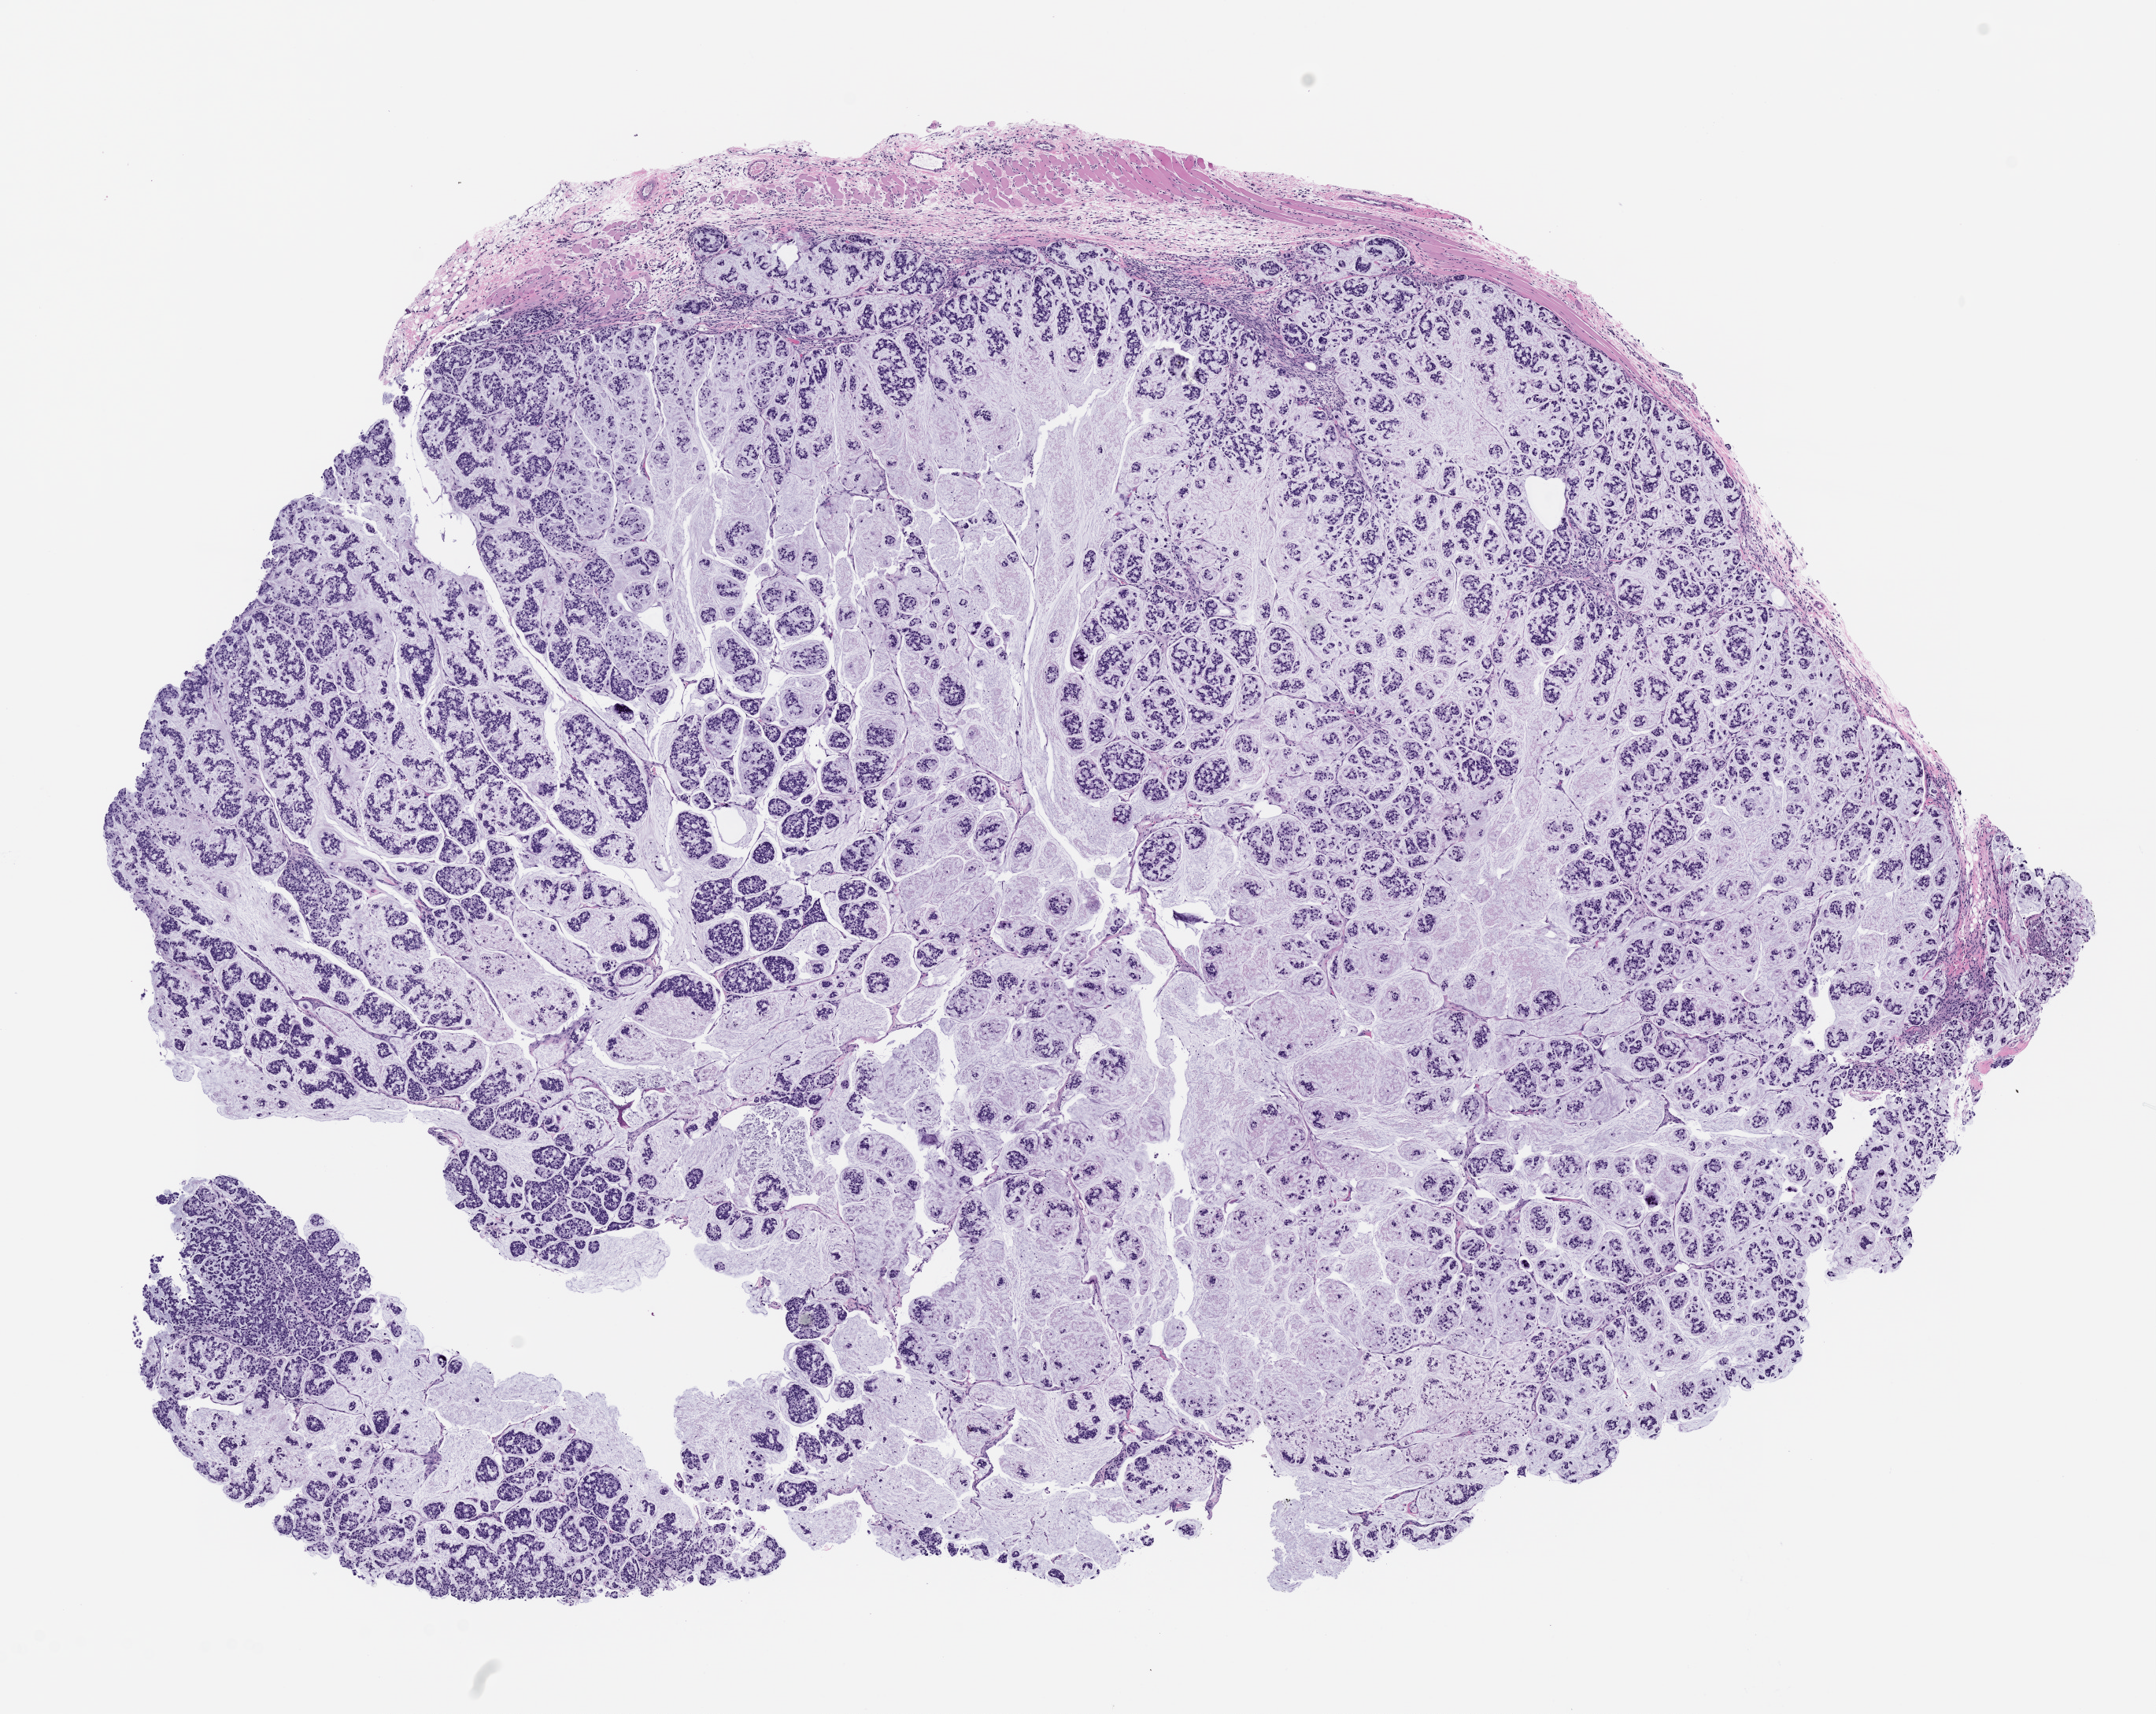
Haematoxylin and eosin whole-slide image of a patient-derived xenograft (PDX) tumor grown in a mouse, passage 1 — low-resolution overview of the scanned area, about 11.0 x 8.8 mm. Formalin-fixed paraffin-embedded section. Tumor site category: colon.
Originating patient diagnosis: Colon Adenocarcinoma.